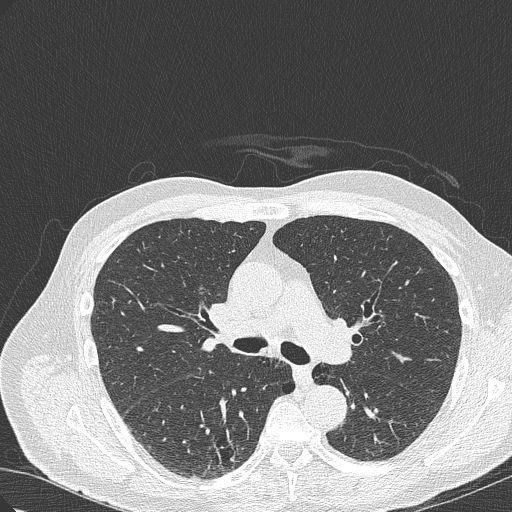
Axial slice from a low-dose chest CT screening exam, first (baseline) screen, lung window (W 1500 / L -600 HU), lung (sharp) reconstruction kernel (B50f). Male participant, aged 70 years at enrolment.
Expert-annotated lung lesion, box from (x=200, y=419) to (x=264, y=470) px. The screening reader recorded 4 non-calcified nodules or masses ≥4 mm on this exam; which of them this box marks is not recorded. Official screen result: positive, change unspecified: nodule(s) >= 4 mm or enlarging nodule(s), mass(es), or other non-specific abnormalities suspicious for lung cancer. Lung cancer was diagnosed 978 days after this screen (after the third annual screen): bronchiolo-alveolar adenocarcinoma, NOS, right lower lobe, poorly differentiated (G3), stage IB (AJCC 6th edition), 30 mm at pathology.